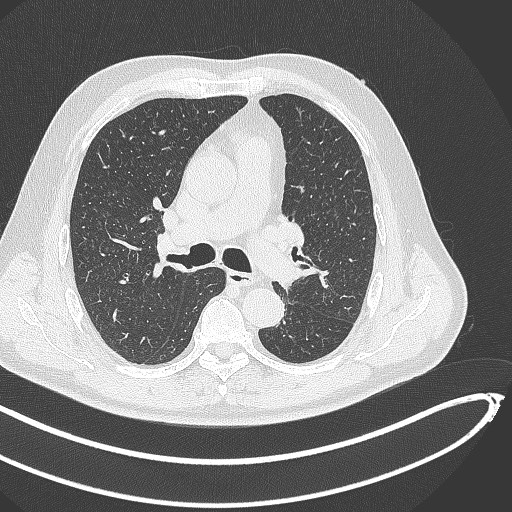
Chest CT, one axial slice; position 288 of 468 along the scan axis; reconstruction kernel B70f; lung window (W 1500 / L -600 HU); 1 mm slice thickness; 512 × 512 image matrix, field of view 400 × 400 mm. Patient: male, 64 years. Case-level facts recorded for this patient, not image findings: clinical TNM (as recorded): T1c N0 M0; histopathological grade: G2.
Annotated regions visible in this slice (rectangle marked by the reading radiologist):
- lung tumour (recorded histology: squamous cell carcinoma): bounding box (x1, y1, x2, y2) in pixels: (276, 265, 308, 287)